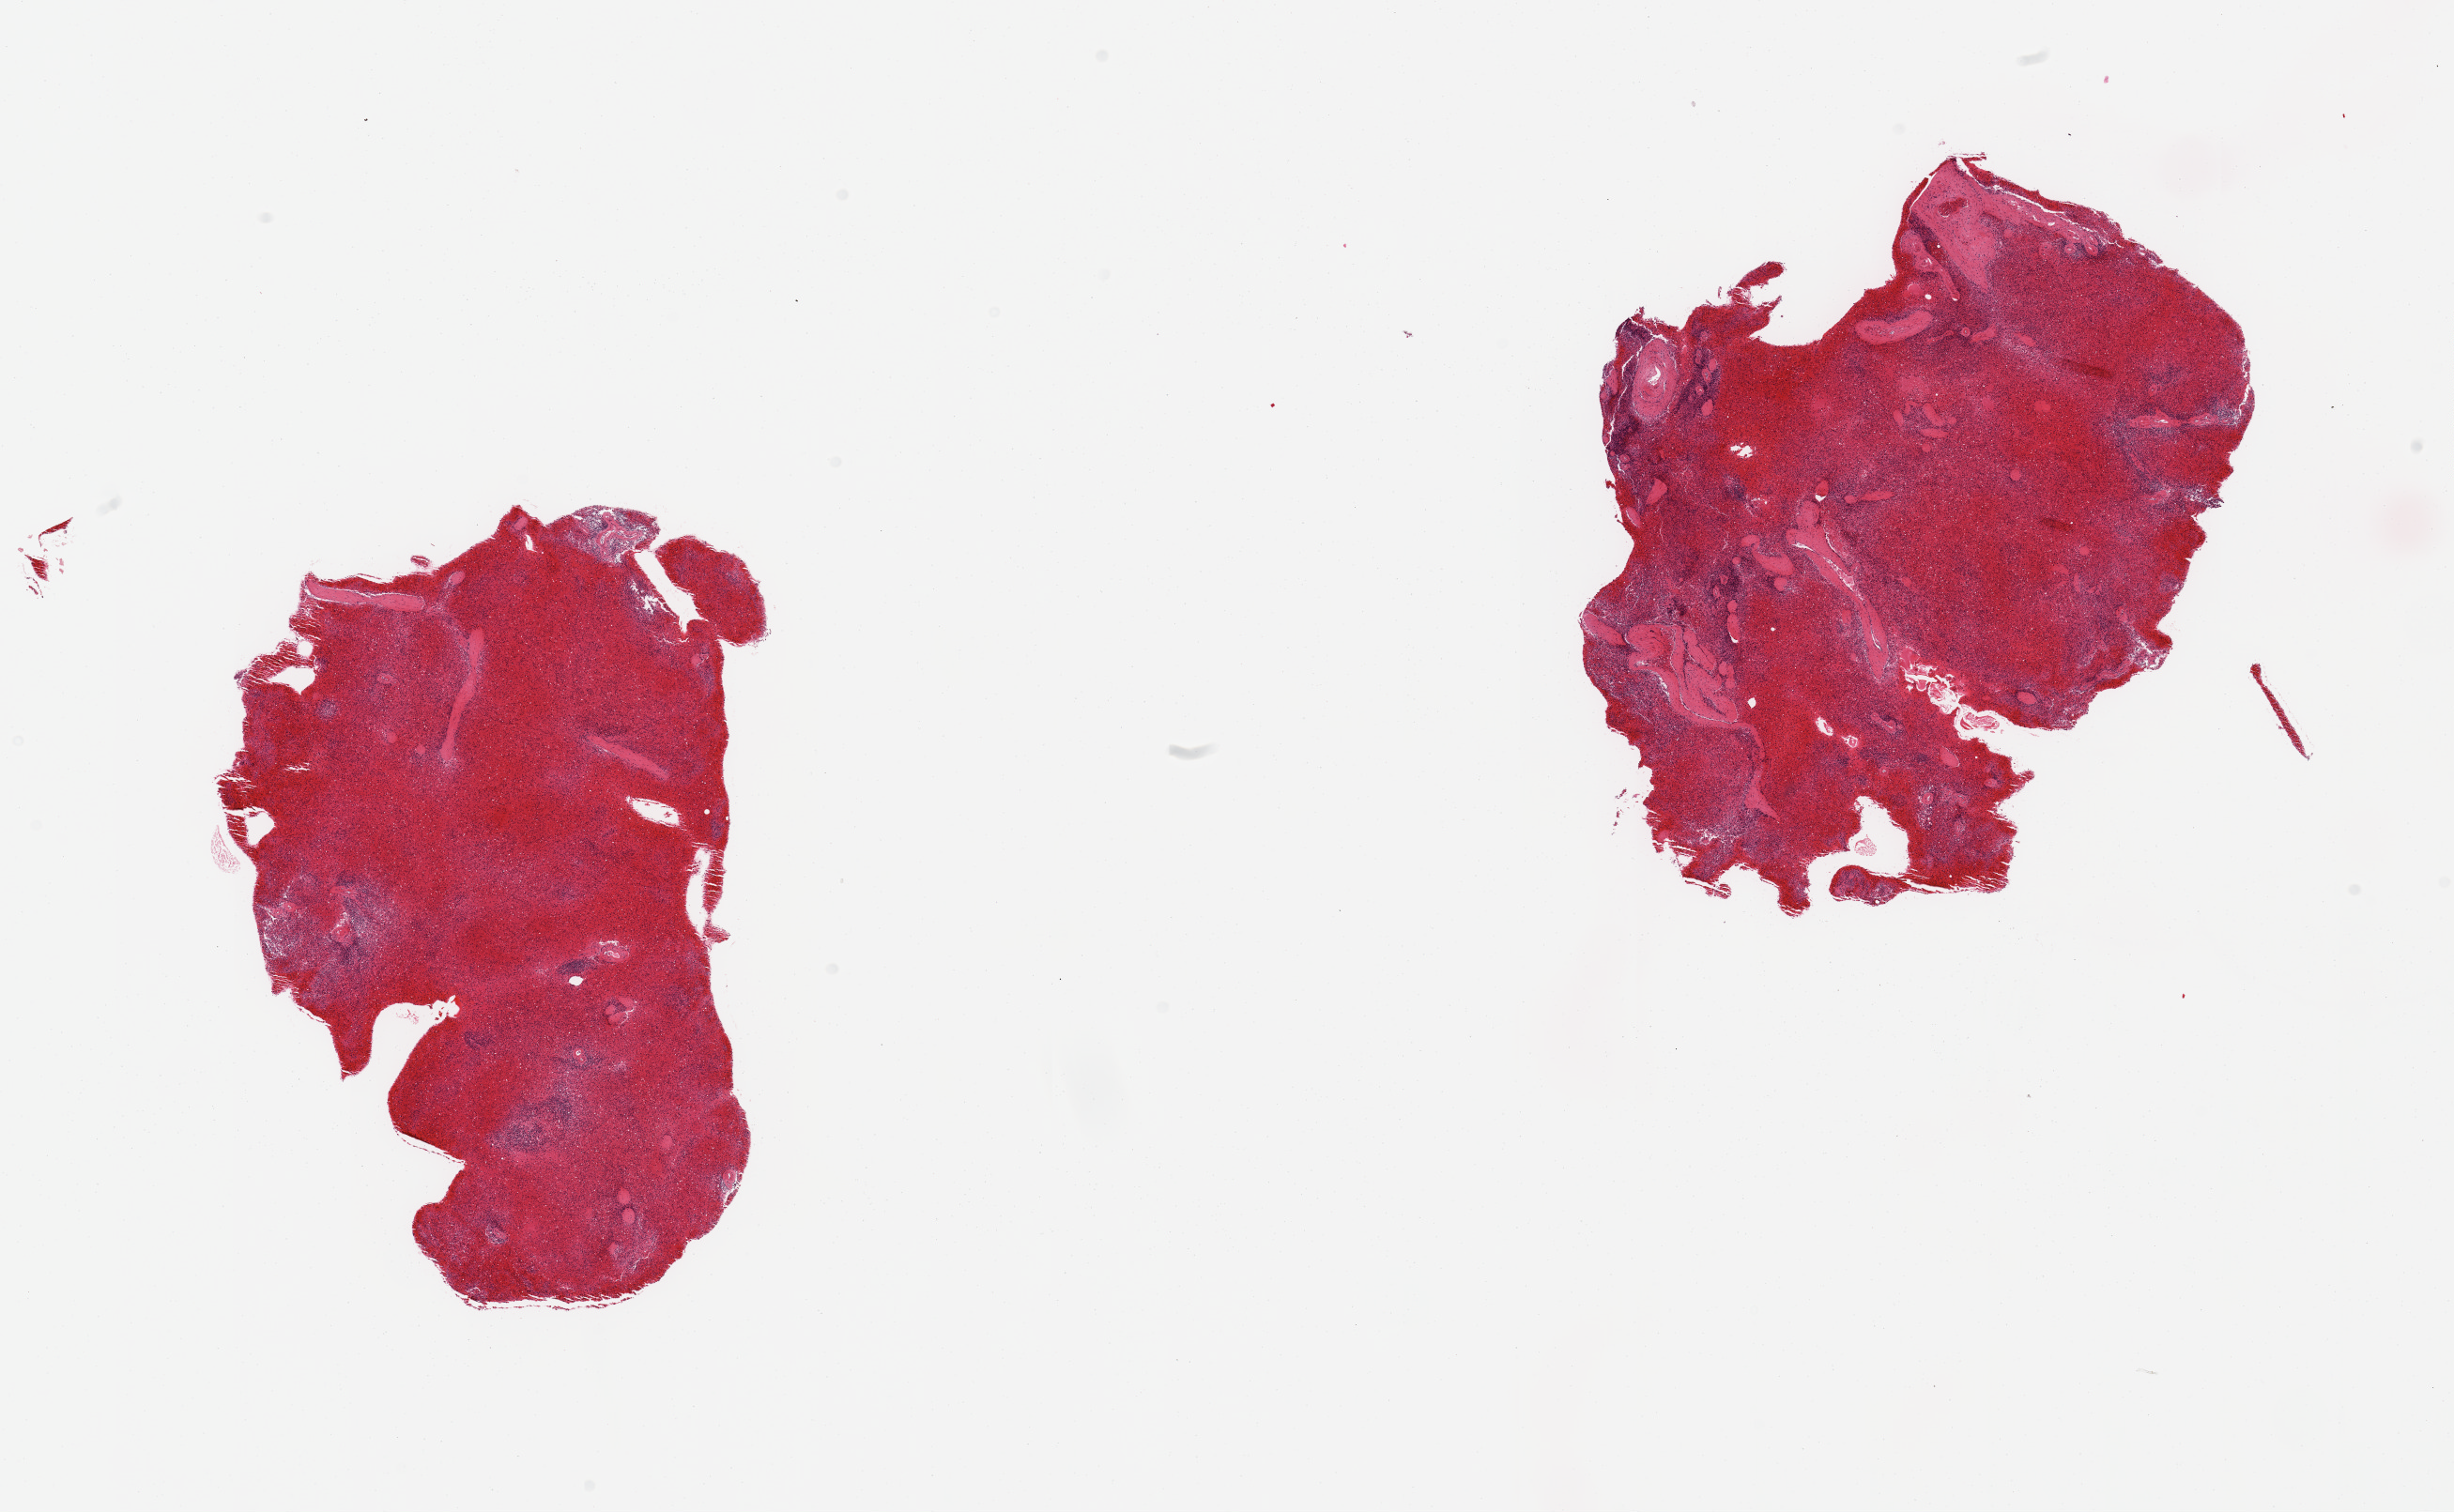
H&E whole-slide image, whole scanned area (about 20.7 x 12.7 mm) shown as a low-resolution overview. PAXgene-fixed paraffin-embedded (PFPE) section. Sampled site (target tissue): spleen. Tissue donor sample. Donor sex: female.
• pathologist's review note for this sample: 2 pieces, marked congestion